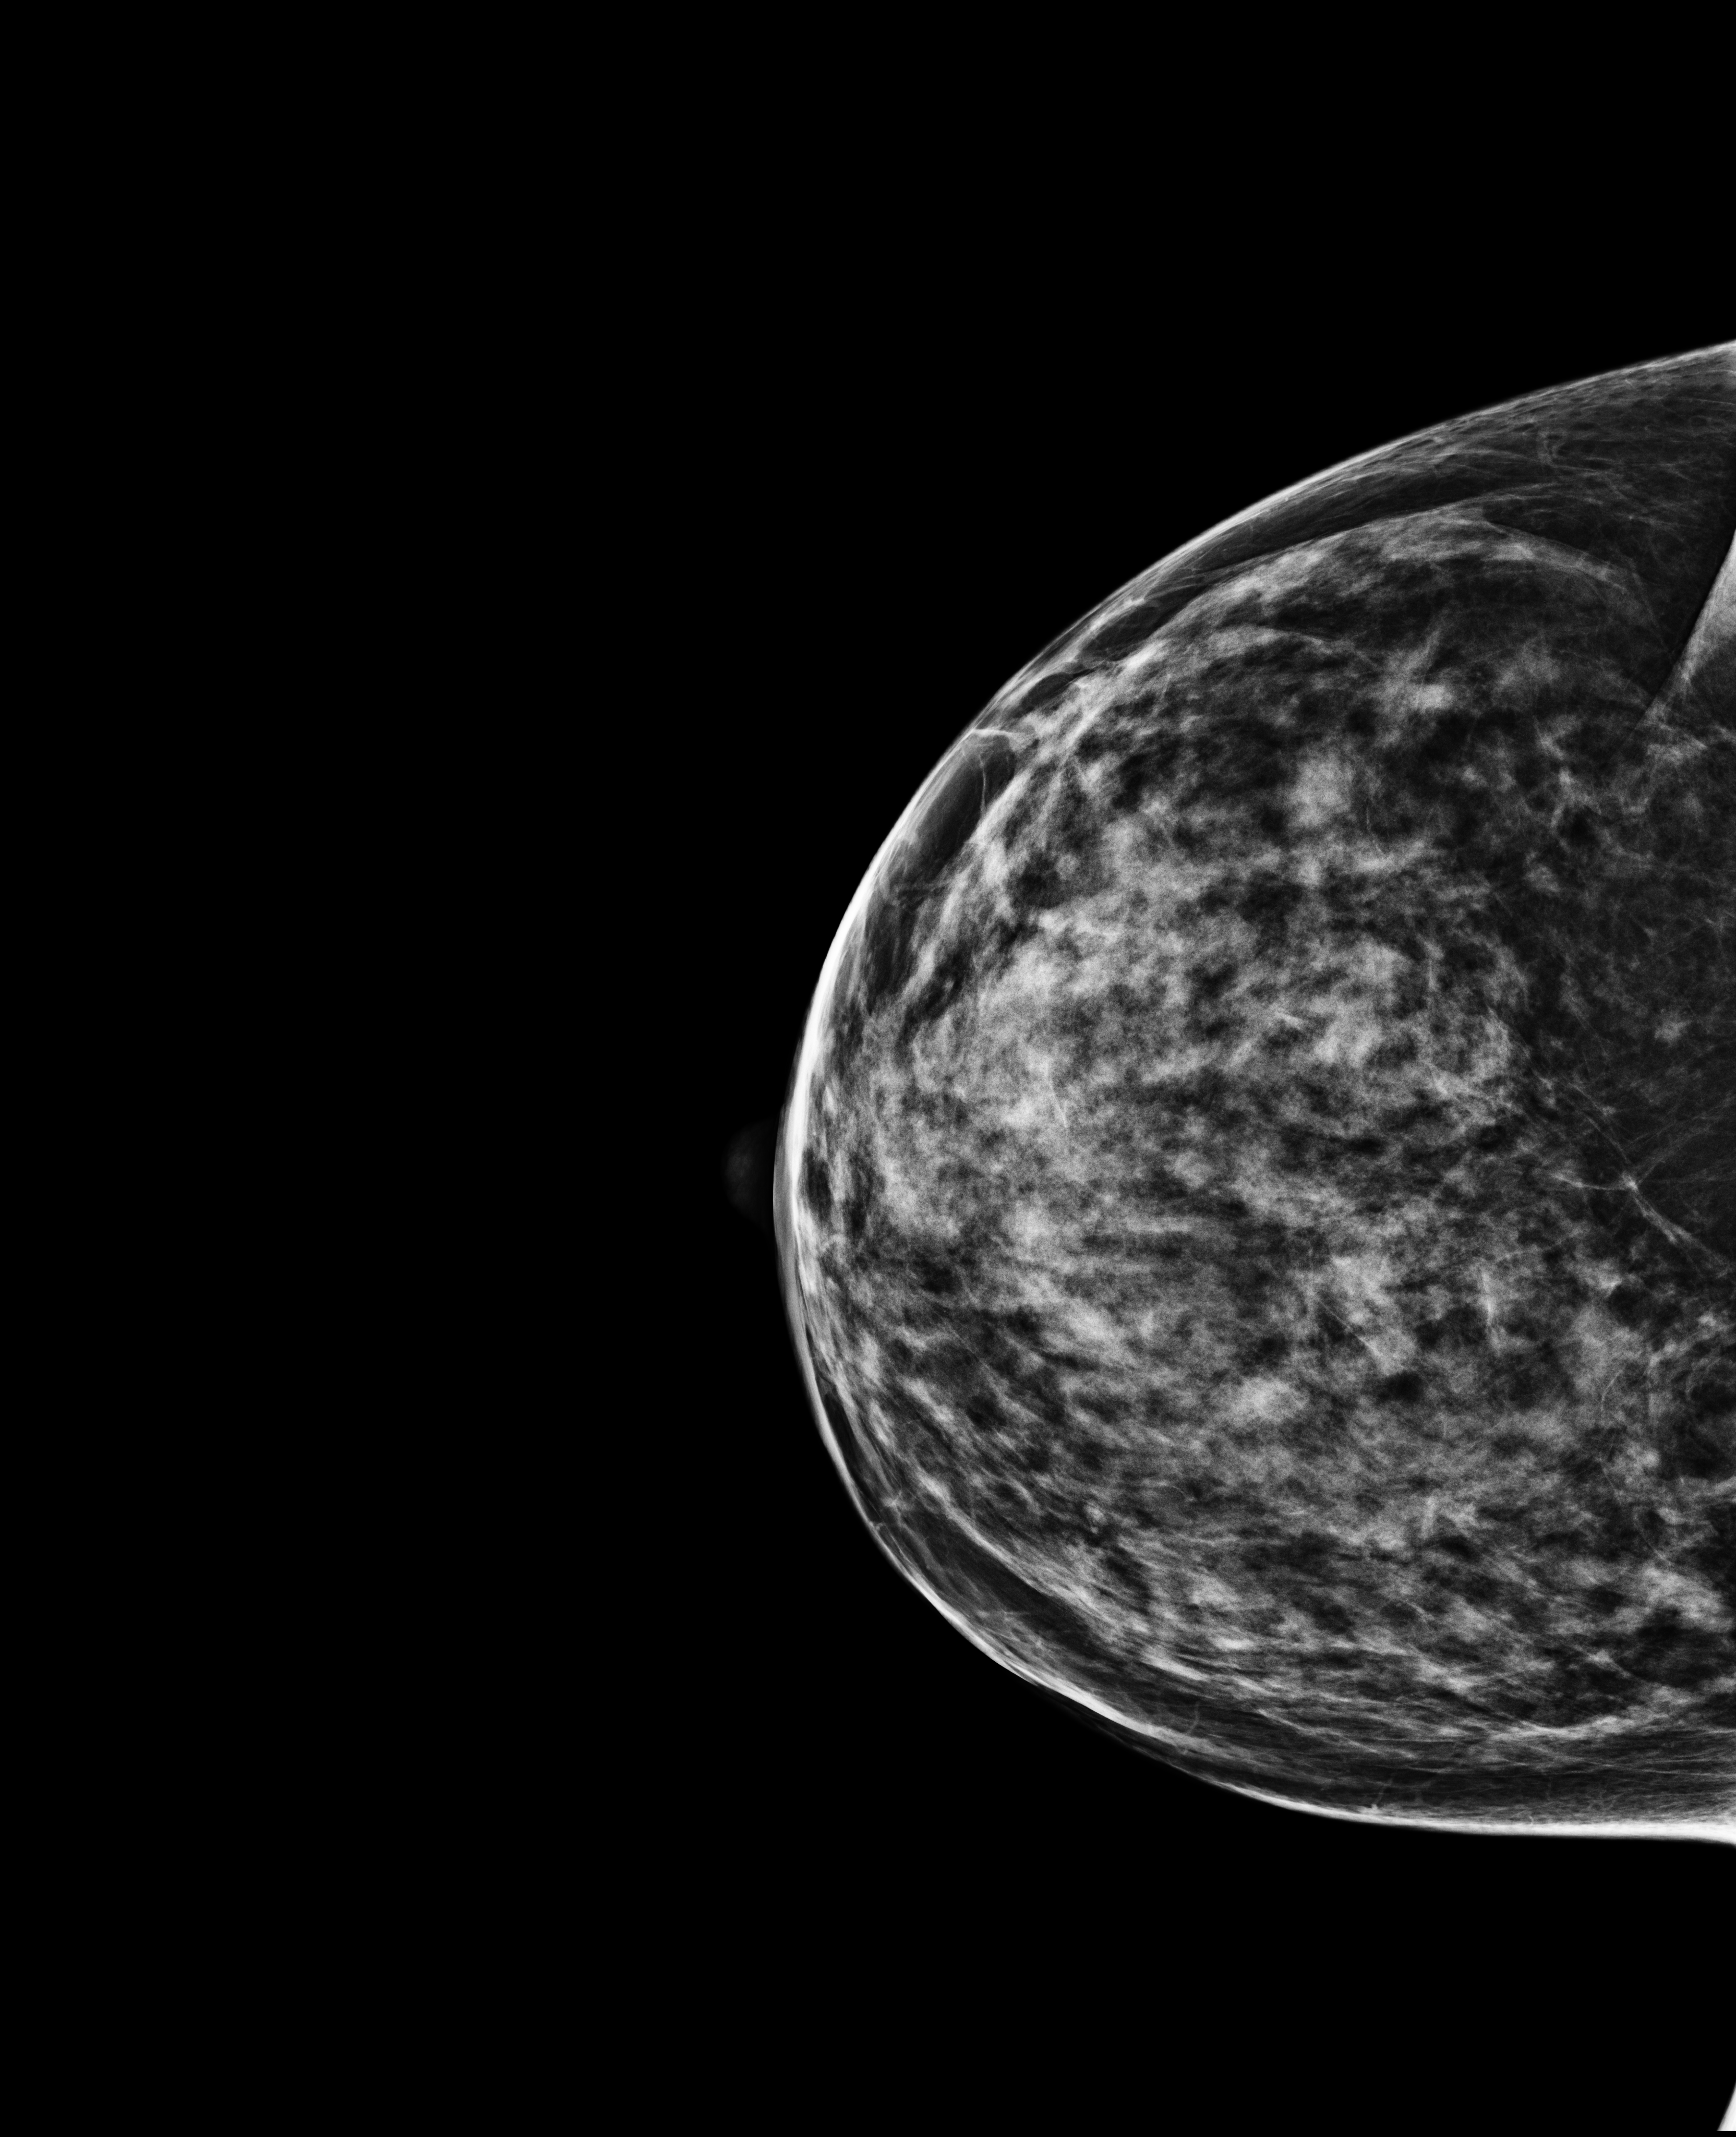
Annual screening mammography examination; system: Selenia Dimensions. Female patient, age 45 years.
Image type: full-field digital mammogram. Breast: right. Projection: craniocaudal (CC) view.